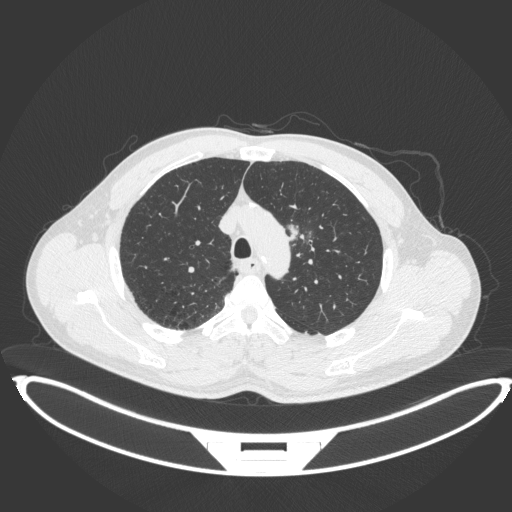
Chest CT, one axial slice. Position 329 of 407 along the scan axis. 120 kVp. Lung window (W 1500 / L -600 HU). 512 × 512 image matrix. Patient: male, 60 years. Case-level facts recorded for this patient, not image findings: clinical TNM (as recorded): T2a N0 M0; histopathological grade: G1-G2.
Annotated regions visible in this slice (bounding box drawn by a radiologist):
- lung tumour (recorded histology: squamous cell carcinoma): bounding box [x1, y1, x2, y2] px = [285, 219, 302, 247]